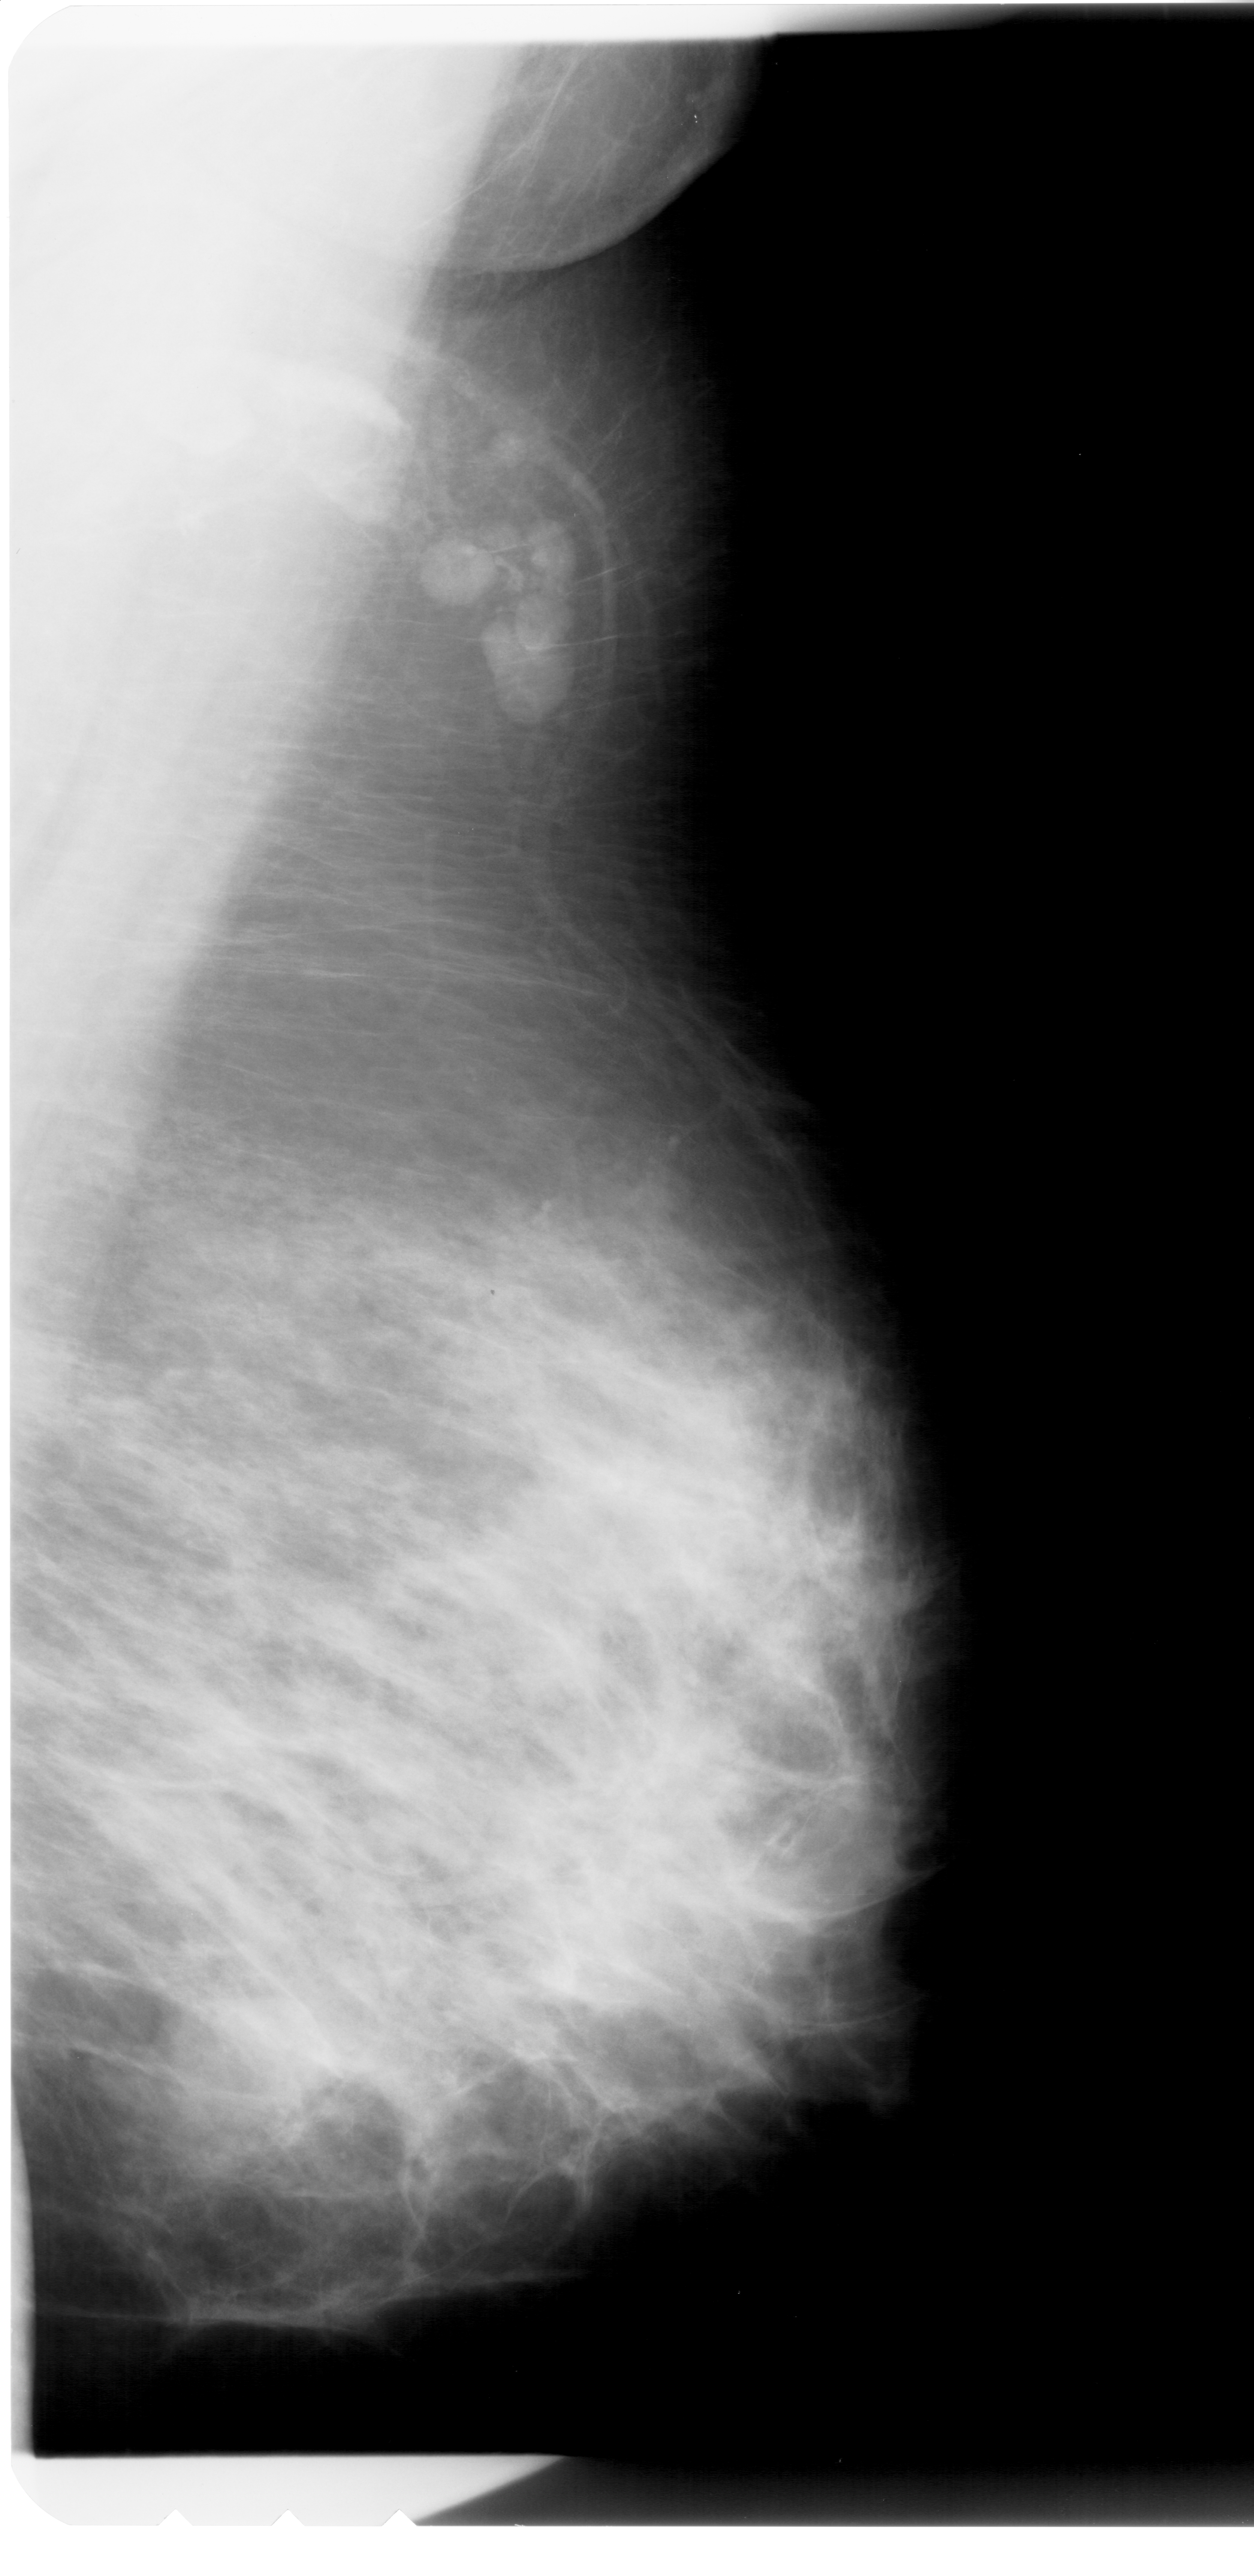
Mammogram (digitized film); right breast; MLO view; BI-RADS breast density category 3 (scale 1–4); 1254 × 2576 image matrix.
Marked abnormalities (boxes around the expert regions of interest):
- mass, shape round, margins obscured; BI-RADS assessment category 4; pathology (as recorded): benign: box from (x=195, y=2000) to (x=348, y=2136) px